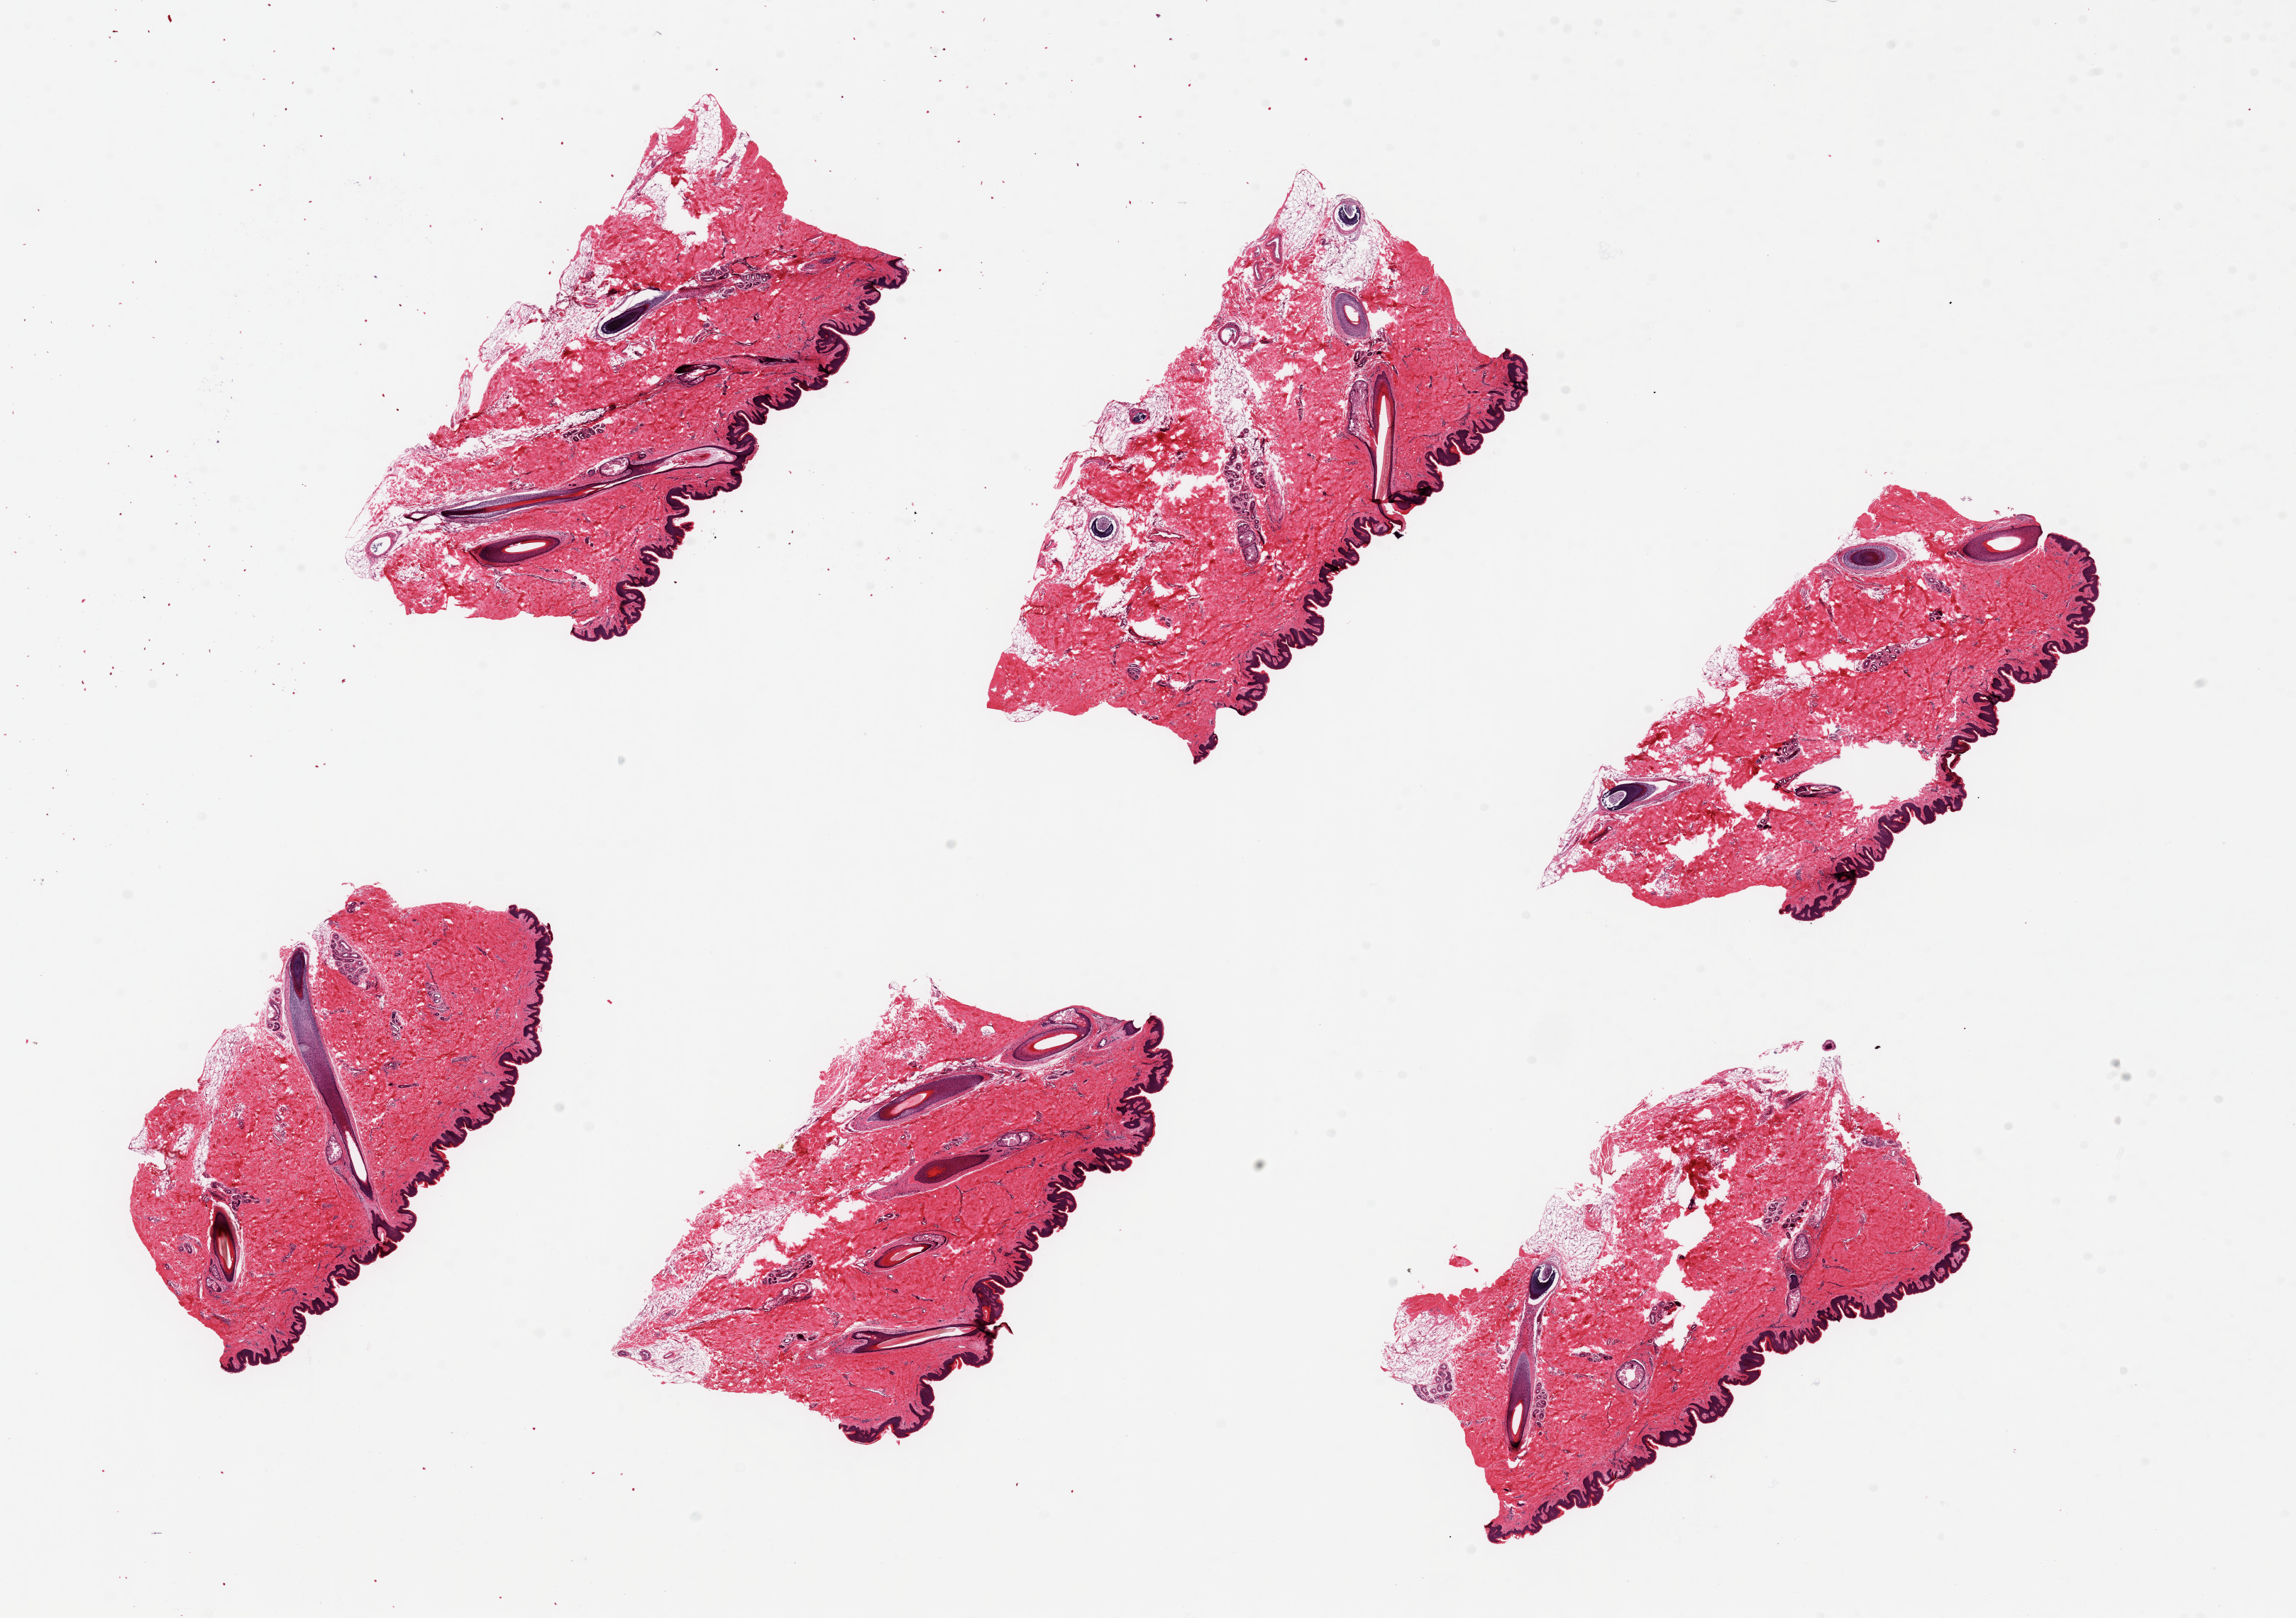
Digitized H&E-stained section — low-resolution overview of the scanned area, about 25.6 x 18.0 mm, PAXgene-fixed, paraffin-embedded tissue, section of skin of suprapubic region (target tissue), donor tissue sample. Donor sex: male.
Pathologist's review note for this sample: 6 pieces ~6x3mm. Squamous epithleium is ~2-3% of thickness.